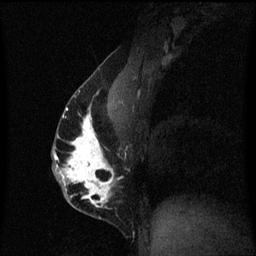
Breast MRI (dynamic contrast-enhanced), one sagittal slice; dynamic contrast-enhanced series, image 2 of 3 at this slice position (ordered by acquisition); 1.5 T; TE 4.2 ms, TR 8.4 ms; 256 × 256 image matrix, field of view 200 × 200 mm. Female patient, age 40 years.
Outlined on this slice (semi-automatic segmentation, software-assisted and operator-edited):
- analysis volume of interest (the breast-tissue region the enhancement analysis was run in; not a lesion): bounding box <53,84,120,211> (left, top, right, bottom; pixels)
- tumour enhancement mask (voxels above the 70 % enhancement threshold inside the analysis volume of interest): <54,94,115,209>